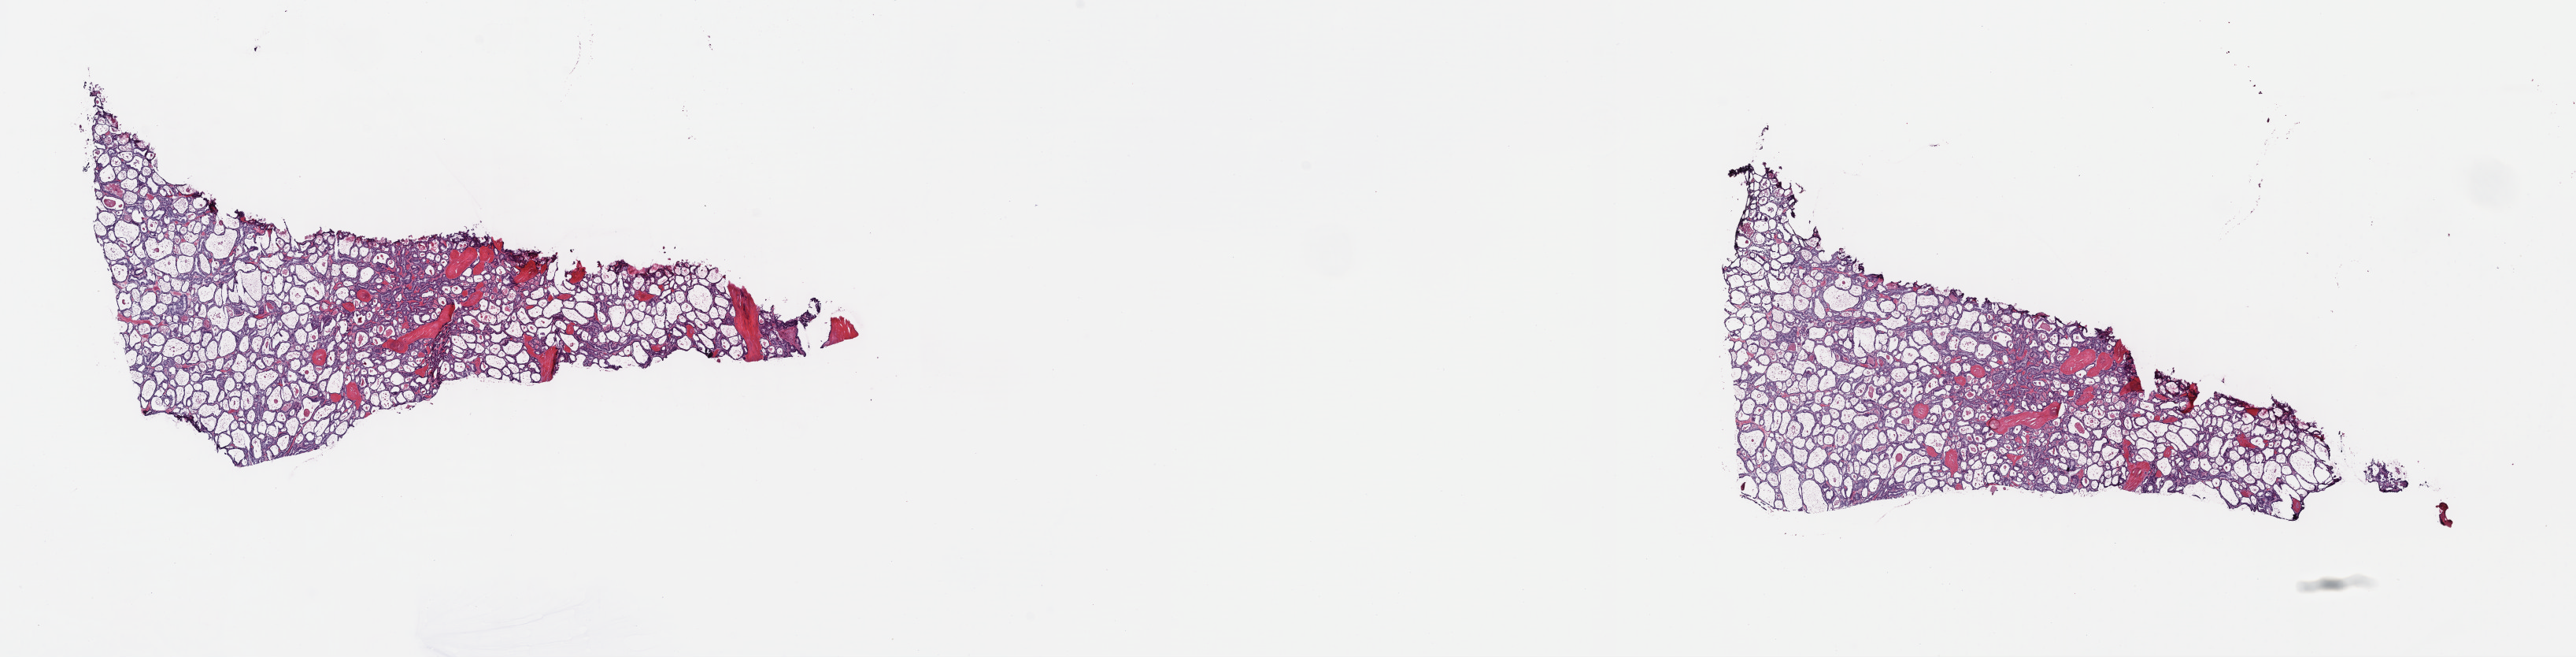
Whole-slide histology image, H&E-stained — a low-resolution overview of the entire scanned area, about 25.7 x 6.6 mm, frozen section from the top of the tissue portion, thyroid, primary tumour sample. Female, age 41 years at initial diagnosis. Composition of this section per pathologist review: tumour cells 90%, tumour nuclei 80%, normal cells 0%, stromal cells 10%, necrosis 0%. Inflammatory infiltration, as recorded: lymphocyte infiltration 2%, monocyte infiltration 1%, neutrophil infiltration 0%.
* lymph nodes positive (case pathology): 1 of 9 examined
* AJCC pathologic stage: I
* diagnosis: Papillary adenocarcinoma, NOS (thyroid gland)